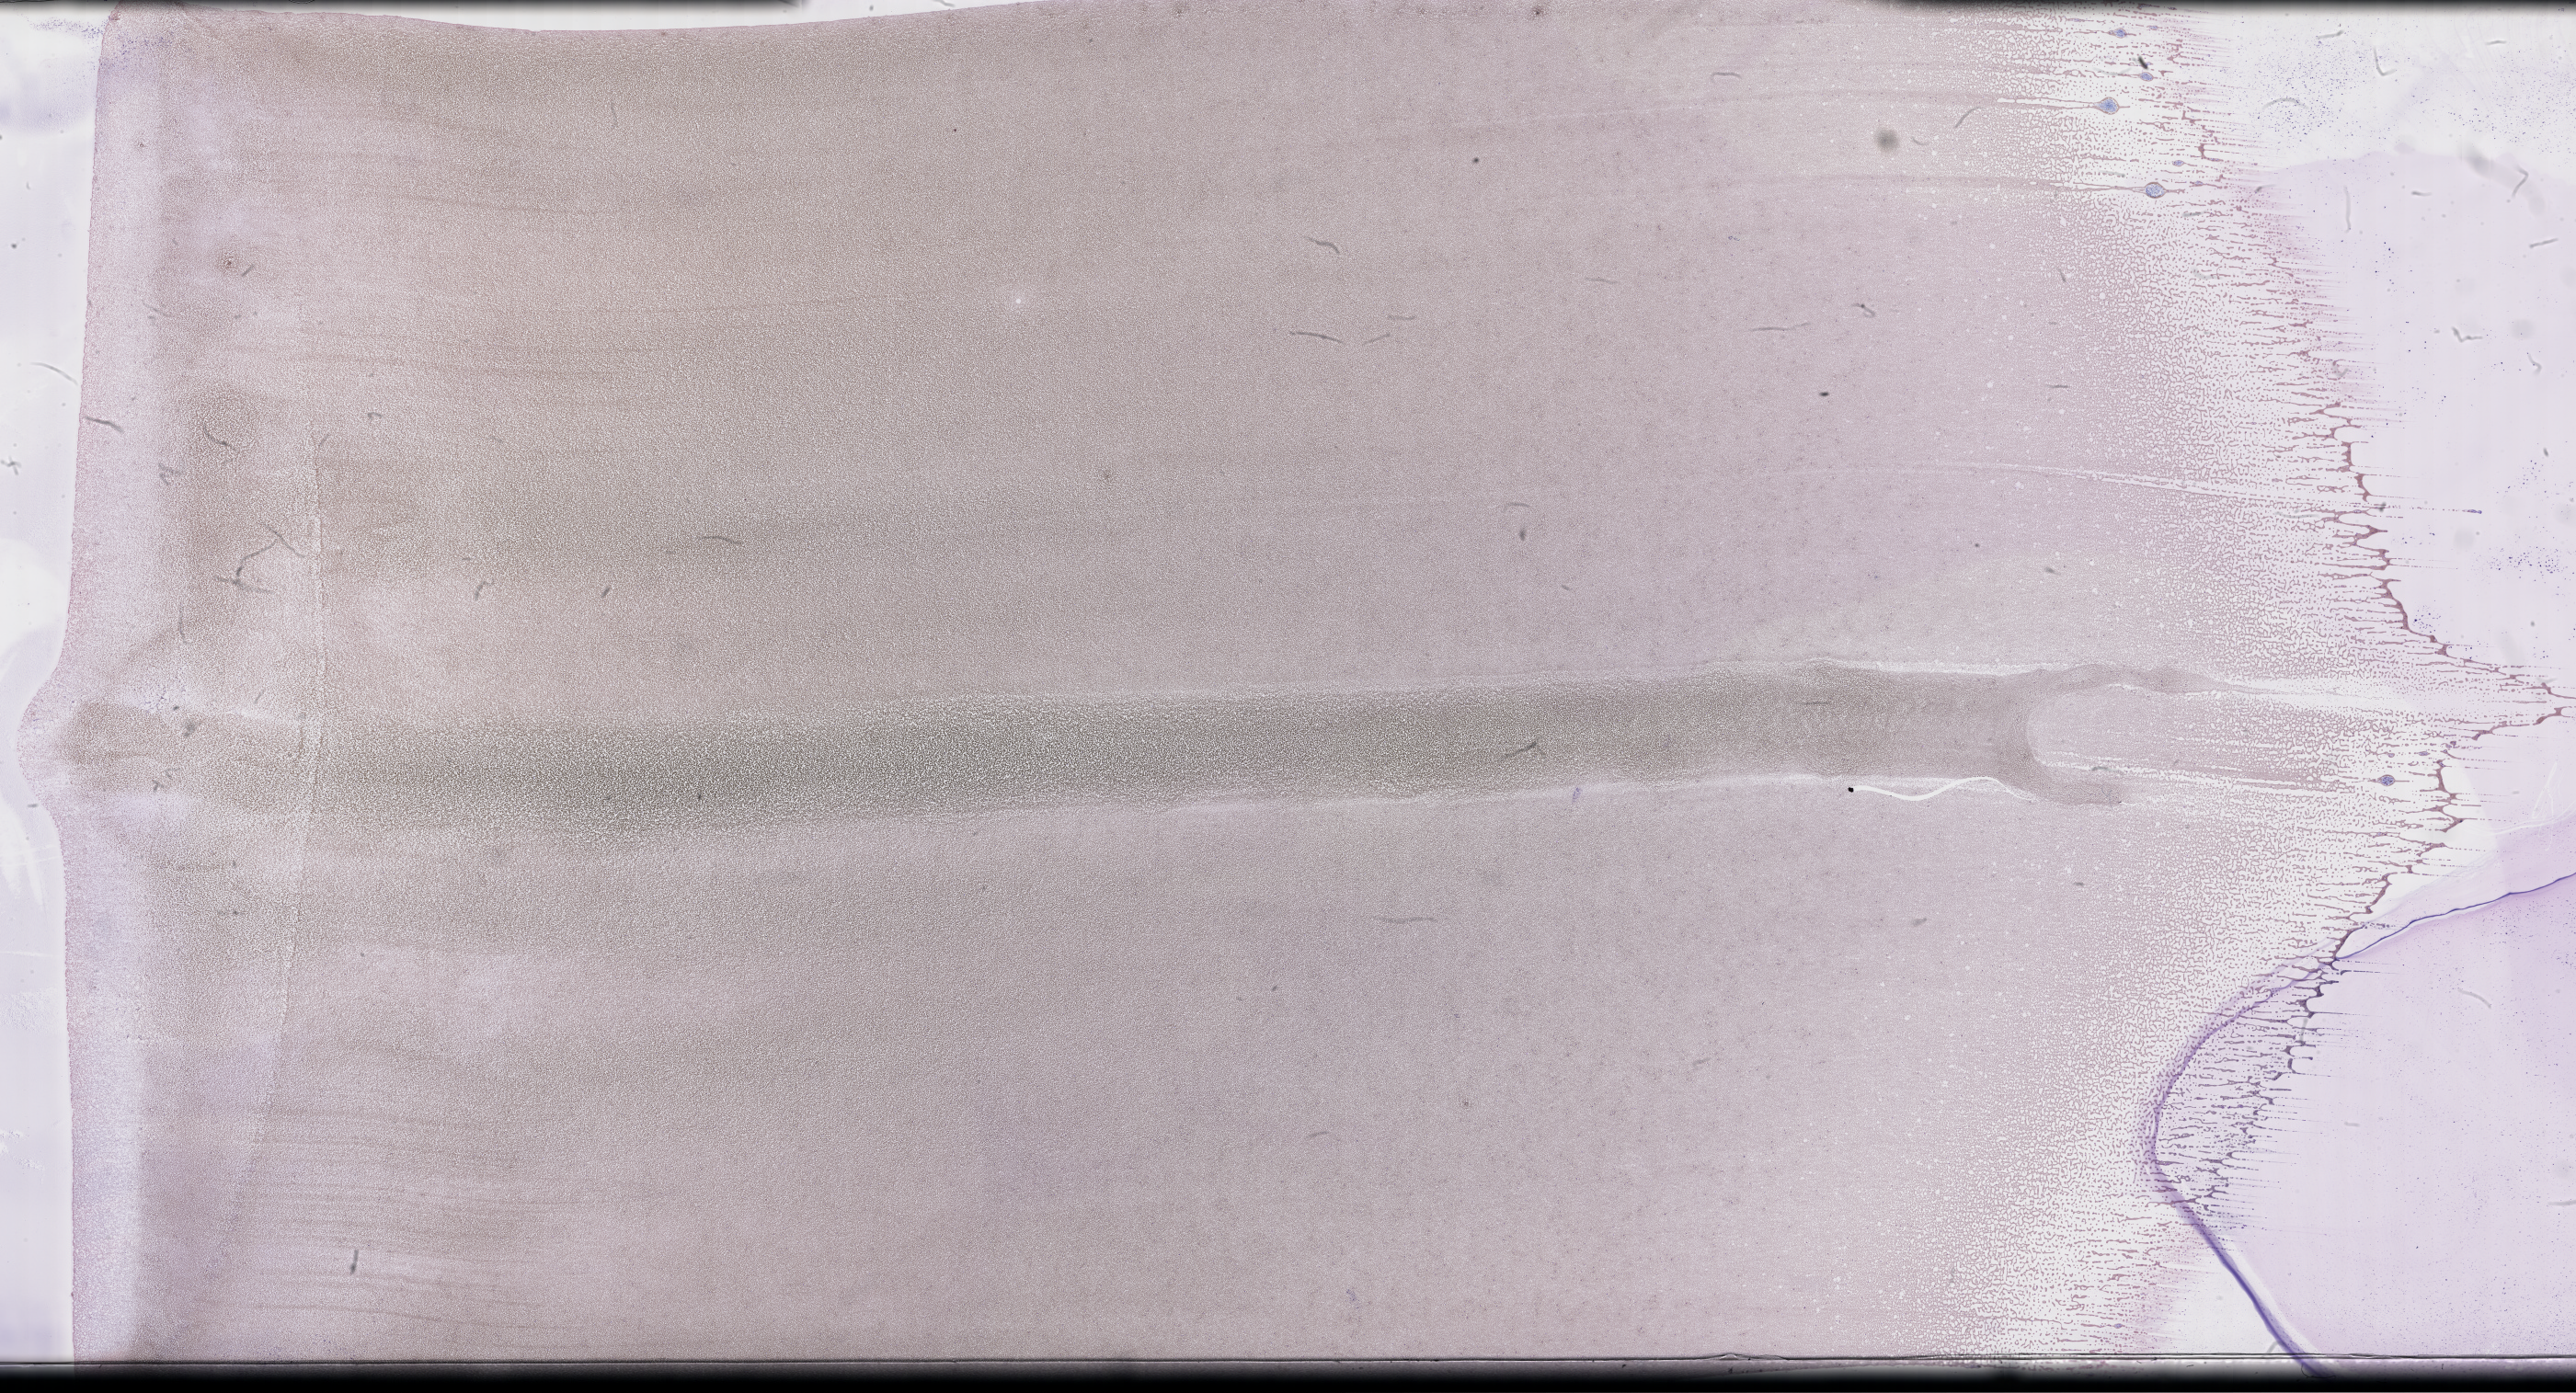
Wright-Giemsa-stained whole blood smear, whole-slide image, shown as a low-resolution overview of the whole scanned area (about 45.2 x 24.5 mm). Smear from an EDTA sample. Collected on treatment. Patient sex: male.
From a patient with: Plasma Cell Myeloma.